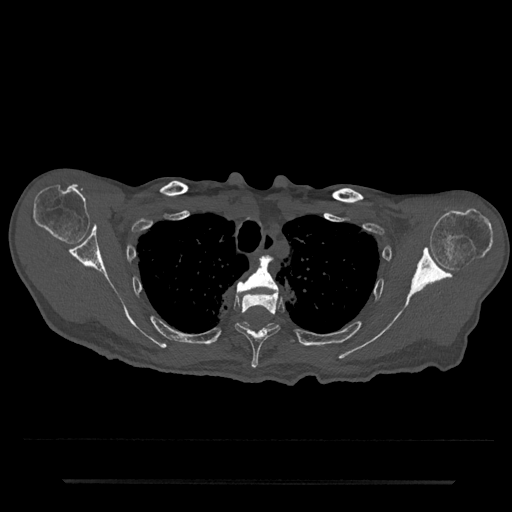
CT including the spine, one axial slice. Position 622 of 797 along the scan axis. Reconstruction kernel Br40s/3. Bone window (W 1800 / L 400 HU). 0.5 mm slice thickness. 512 × 512 image matrix, field of view 427 × 427 mm. Patient: male, 74 years. From the clinical record (not read from this slice): primary cancer: prostate.
Structures marked on this image (semi-automatically segmented with operator editing):
- T3 vertebra: bounding box [x1, y1, x2, y2] px = [236, 257, 279, 294]
- T4 vertebra: [235, 292, 280, 368]
- T5 vertebra: [242, 322, 295, 344]